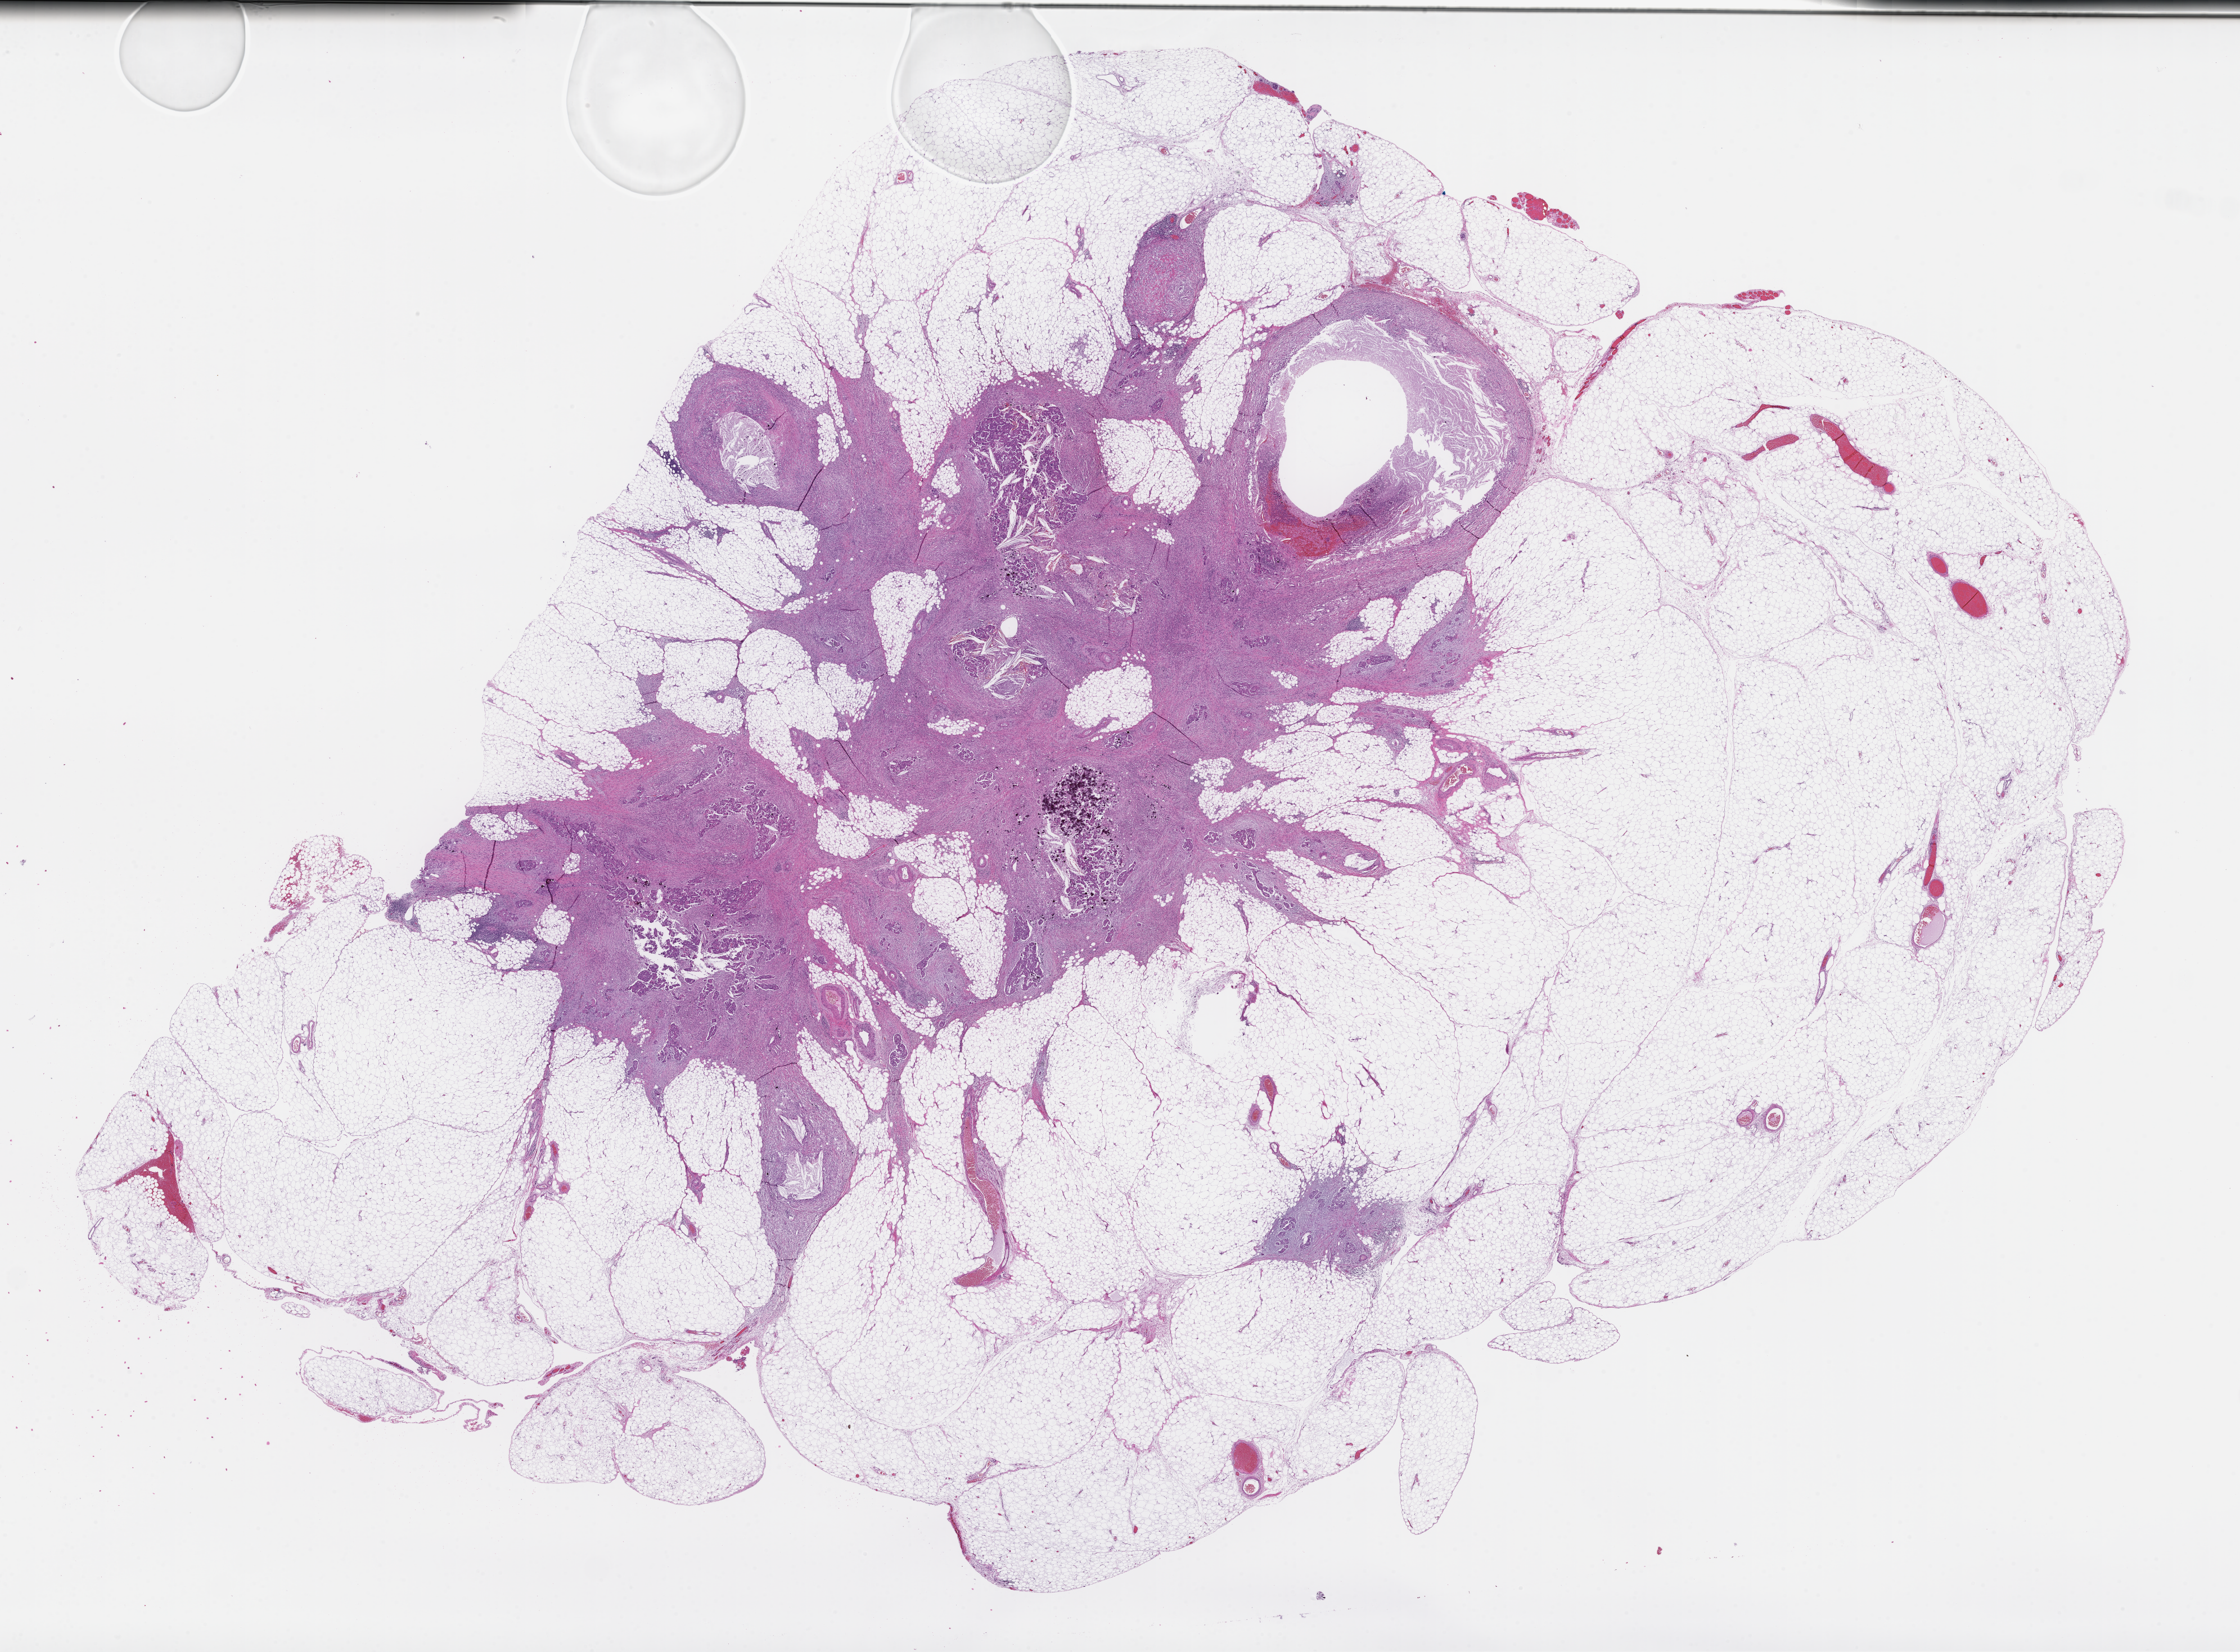
Digitized haematoxylin and eosin-stained section, whole scanned area (about 32.2 x 23.7 mm) shown as a low-resolution overview. Formalin-fixed paraffin-embedded section. Tissue site: omentum. Specimen time point: collected on treatment. Patient: female.
This section: primary tumor. Diagnosis: Ovarian Carcinoma.